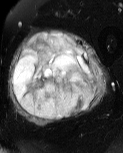
MRI of an extremity soft-tissue mass, one axial slice; position 26 of 60 along the scan axis; T2-weighted fat-saturated; MR volume resampled by the dataset authors to the PET/CT grid (not the native acquisition matrix); 123 × 153 image matrix. Male patient. From the clinical record (not read from this slice): histological type: pleiomorphic liposarcoma; grade: high; site of the primary tumour: left thigh.
Annotated regions visible in this slice (expert contour drawn on MRI and transferred to this co-registered scan by the dataset authors):
- gross tumour volume including surrounding oedema: box from (x=8, y=29) to (x=108, y=126) px
- gross tumour volume (mass): (x=13, y=33)–(x=96, y=121)